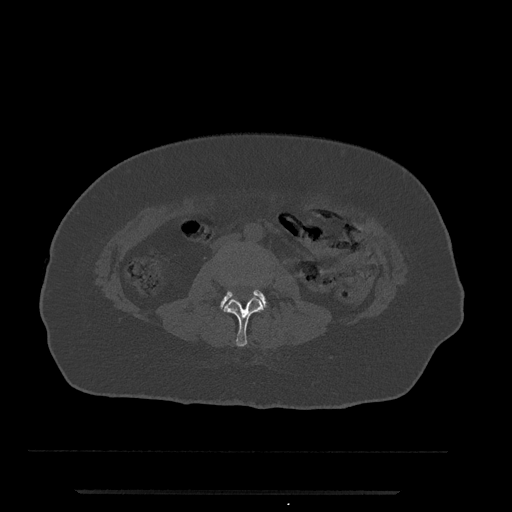
CT including the spine, one axial slice. Position 6 of 797 along the scan axis. Bone window (W 1800 / L 400 HU). 512 × 512 image matrix, field of view 440 × 440 mm. Female patient, age 51 years. From the clinical record (not read from this slice): primary cancer: neuro.
Annotated regions visible in this slice (semi-automatically segmented with operator editing):
- L2 vertebra: bounding box (x1, y1, x2, y2) in pixels: (224, 281, 264, 347)